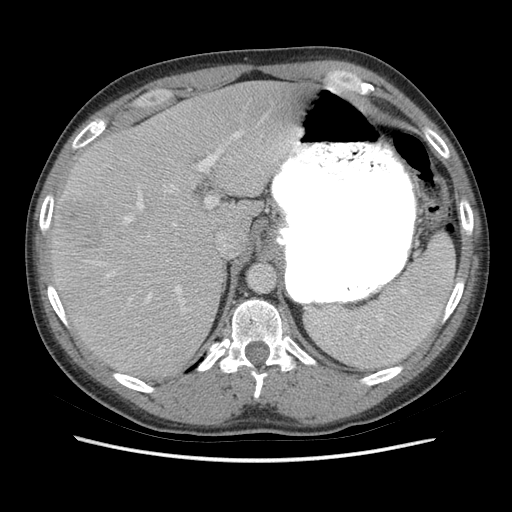
Contrast-enhanced abdominal CT (liver protocol), one axial slice; slice 49 of 73 in the series (ordered by position); reconstruction kernel STANDARD; soft-tissue window (W 400 / L 40 HU); 2.5 mm slice thickness; 512 × 512 image matrix. From the clinical record (not read from this slice): diagnosis: hepatocellular carcinoma (patient treated with transarterial chemoembolisation; whether this scan precedes or follows treatment is not stated here); TNM stage (as recorded): Stage-IIIA; Child-Pugh class: A.
Structures marked on this image (semi-automatically segmented with operator editing):
- liver parenchyma outside the tumour (the mass and vessels are separate outlines, so this box may not span the whole liver): bounding box (x1, y1, x2, y2) in pixels: (50, 80, 300, 378)
- mass: (58, 197, 102, 252)
- liver vessels: (66, 129, 300, 303)